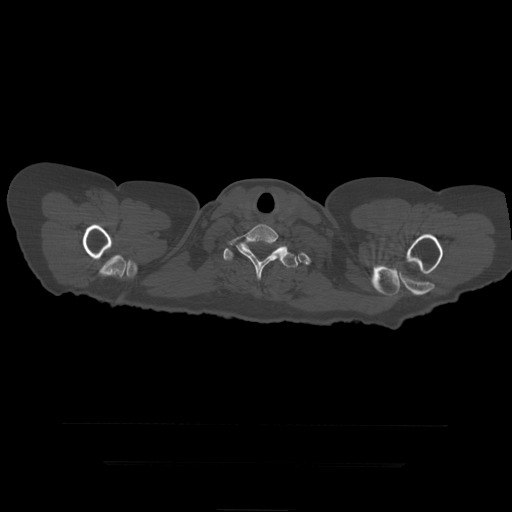
CT including the spine, one axial slice. Position 384 of 399 along the scan axis. Reconstruction kernel STANDARD. 120 kVp. Bone window (W 1800 / L 400 HU). 512 × 512 image matrix. Patient age 41 years. From the clinical record (not read from this slice): primary cancer: breast.
Annotated regions visible in this slice (semi-automatically segmented with operator editing):
- T1 vertebra: bounding box <229,224,291,281> (left, top, right, bottom; pixels)
- T2 vertebra: <224,242,299,268>